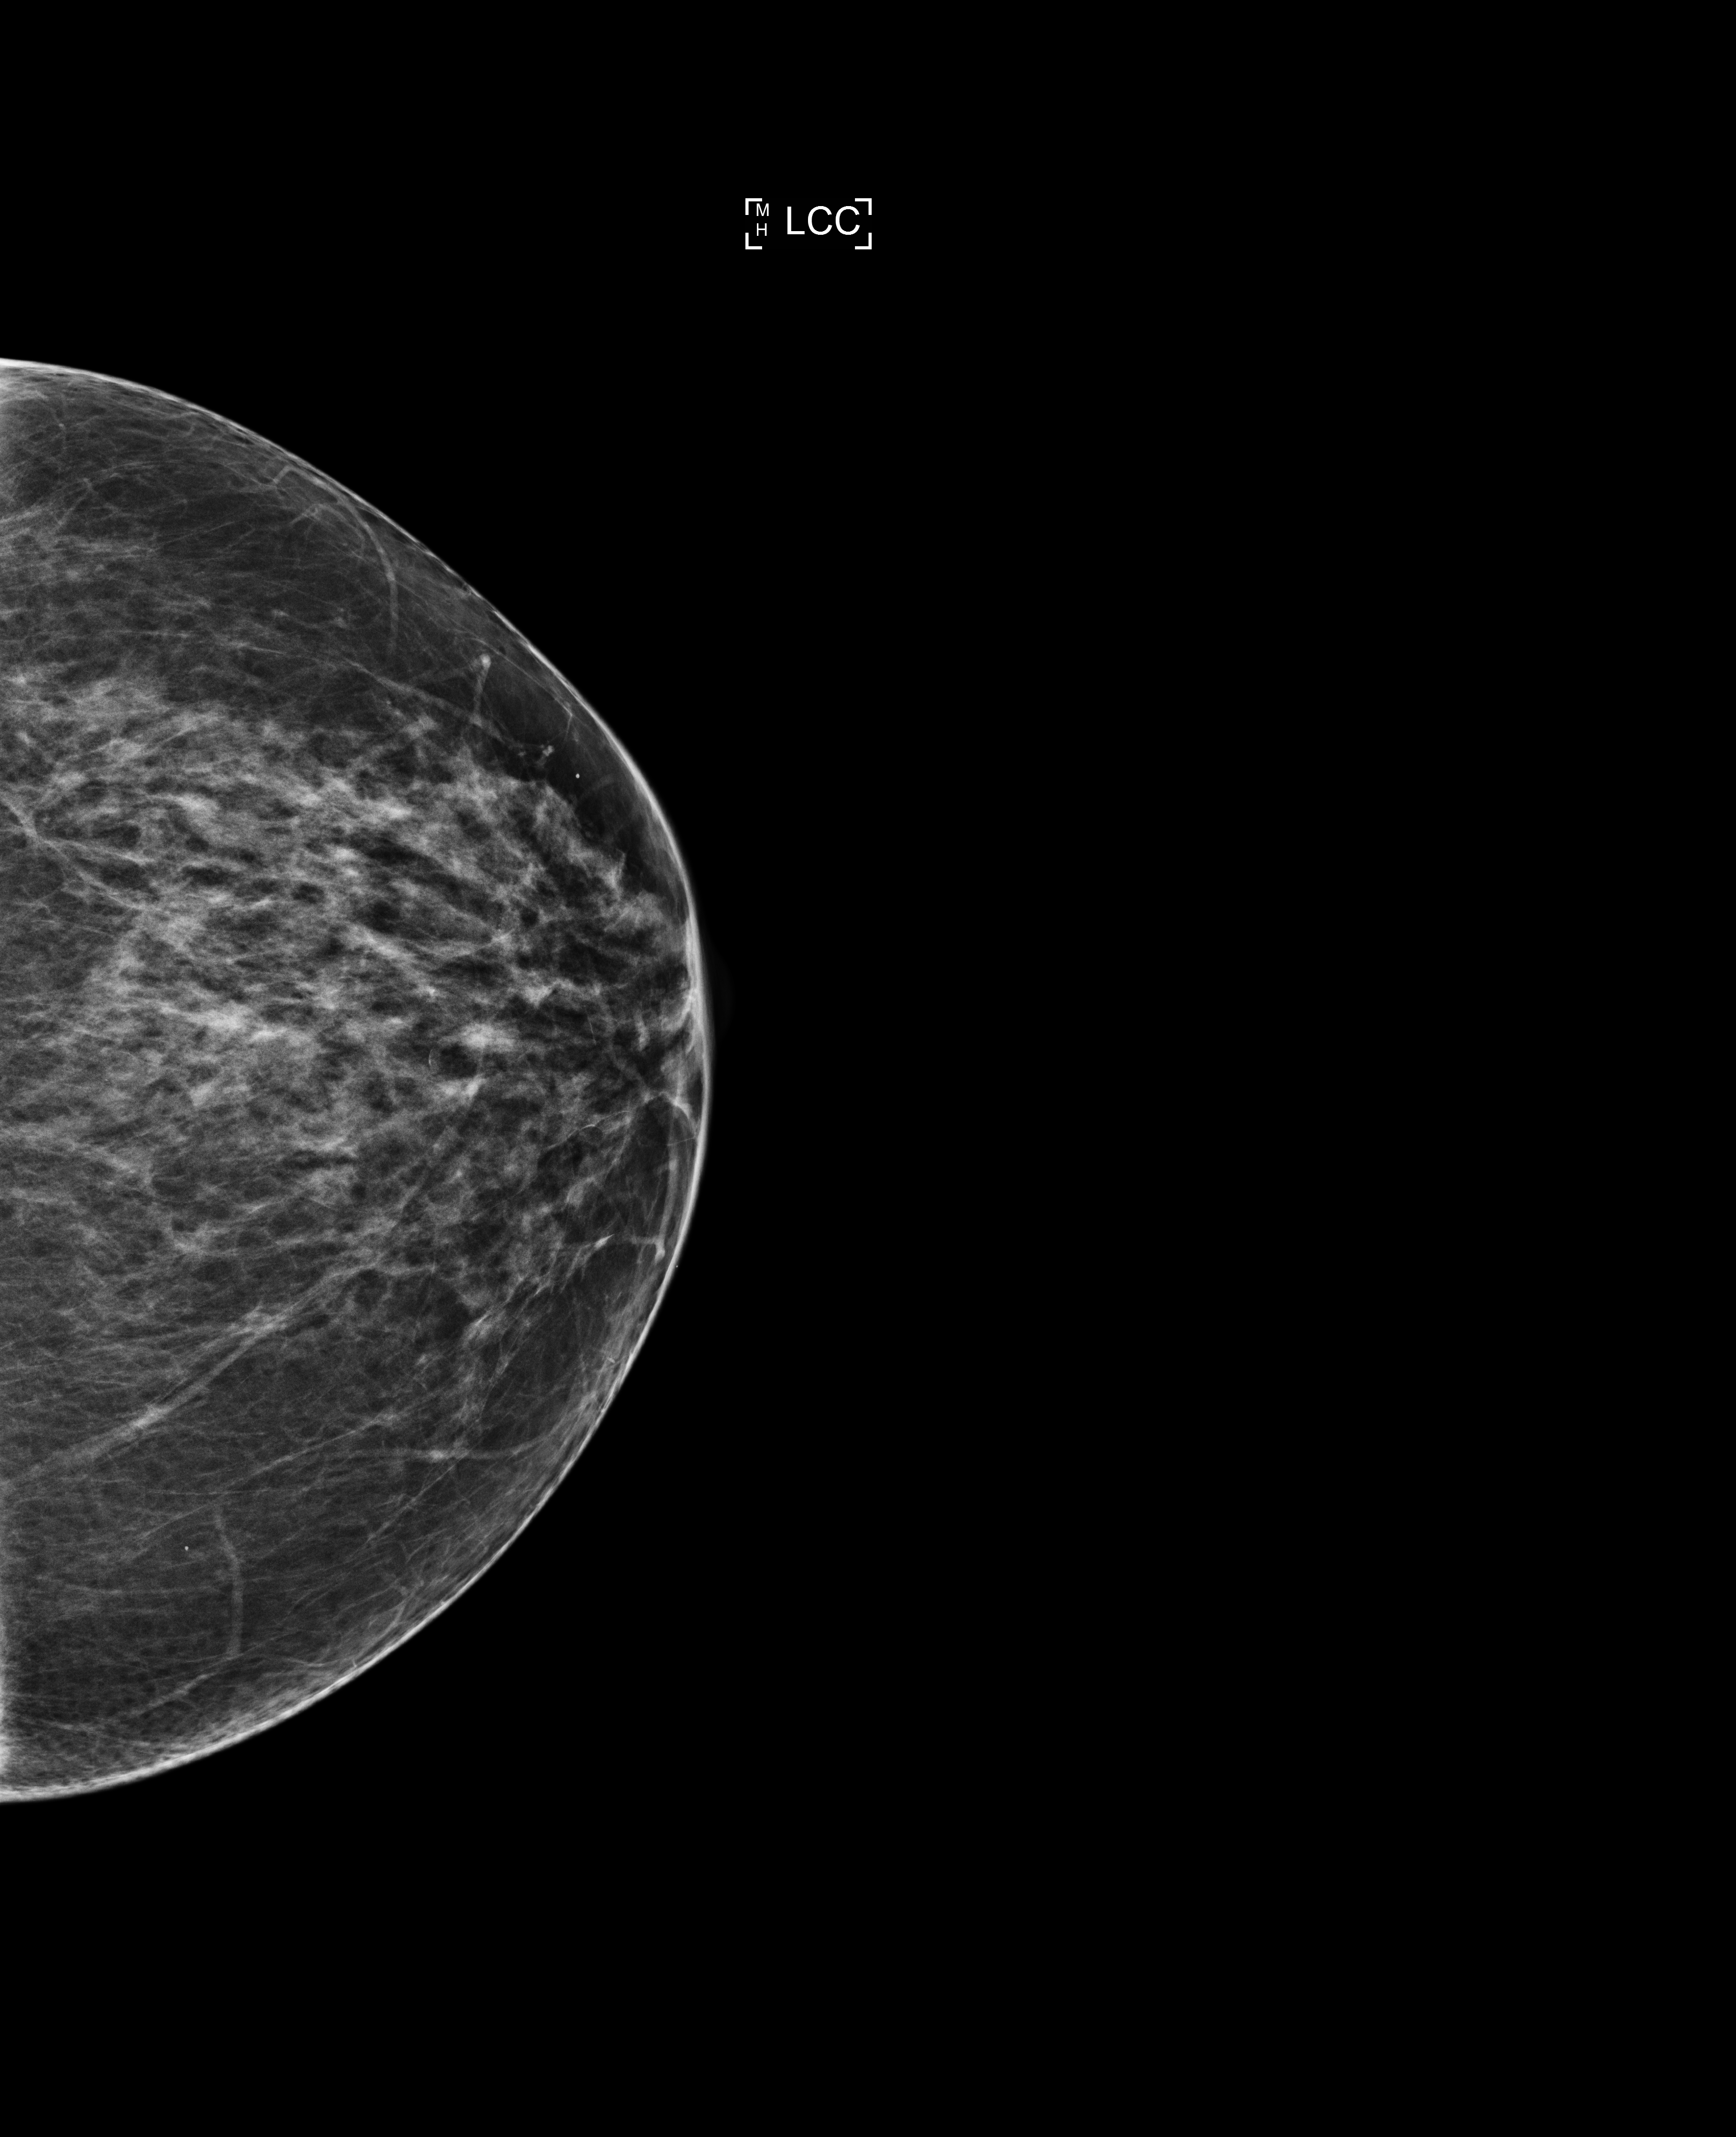
Annual screening mammography examination. Patient aged 70 years (female).
Image type: full-field digital mammogram. Breast: left. Projection: craniocaudal (CC) view. BI-RADS breast density category at the screening exam (both breasts, scale 1–4): 2. Final BI-RADS assessment for this screening round (tomosynthesis exam, both breasts): category 1. Recall: no recall after this screen.